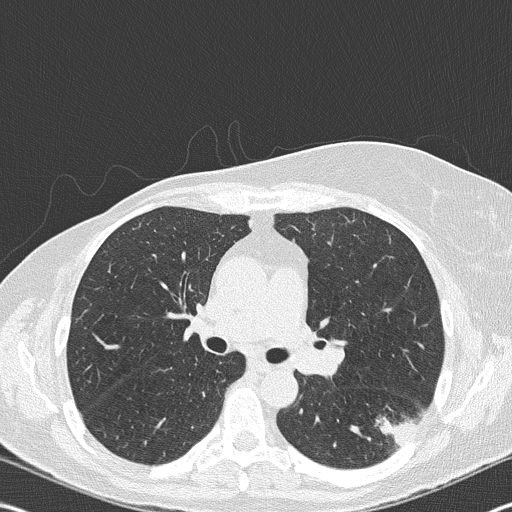
Low-dose screening chest CT, one axial slice; position 110 of 177 along the scan axis; reconstruction kernel B50f; 120 kVp; lung window (W 1500 / L -600 HU); 2 mm slice thickness; 512 × 512 image matrix, field of view 342 × 342 mm.
Annotated regions visible in this slice (expert manual segmentation):
- lesion 1 (tumor): bounding box (x1, y1, x2, y2) in pixels: (376, 413, 422, 447)
- lesion 2 (nodule, hilum of left lung): (297, 346, 343, 375)